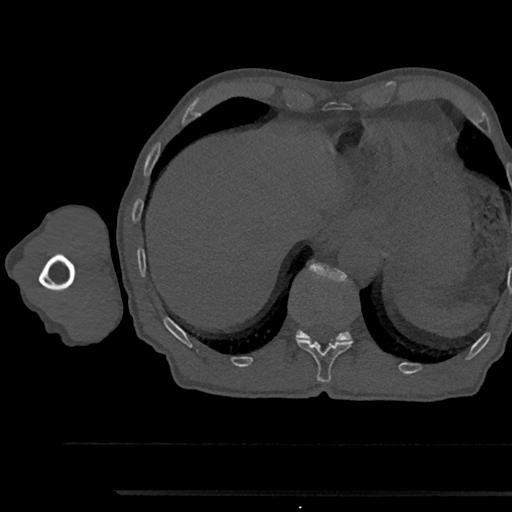
CT including the spine, one axial slice. Position 759 of 797 along the scan axis. Bone window (W 1800 / L 400 HU). 0.5 mm slice thickness. 512 × 512 image matrix. Patient: male, 79 years. From the clinical record (not read from this slice): primary cancer: prostate.
Annotated regions visible in this slice (semi-automatically segmented with operator editing):
- T11 vertebra: box from (x=296, y=338) to (x=352, y=383) px
- T12 vertebra: (x=295, y=264)–(x=352, y=342)